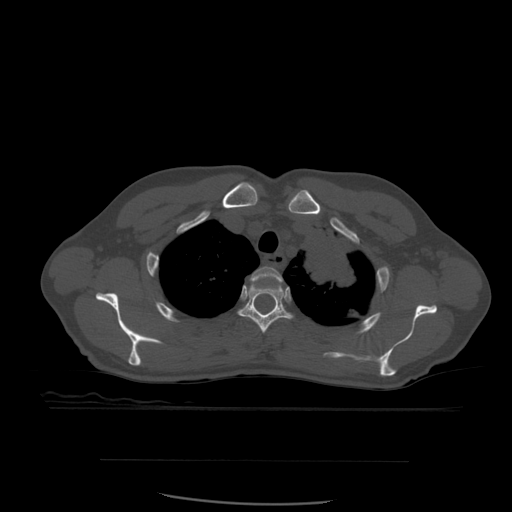
CT including the spine, one axial slice. Bone window (W 1800 / L 400 HU). 1.25 mm slice thickness. 512 × 512 image matrix. Patient age 48 years. Case-level facts recorded for this patient, not image findings: primary cancer: lung.
Annotated regions visible in this slice (semi-automatically segmented with operator editing):
- T2 vertebra: bounding box [x1, y1, x2, y2] px = [251, 267, 283, 290]
- T3 vertebra: [238, 283, 293, 334]